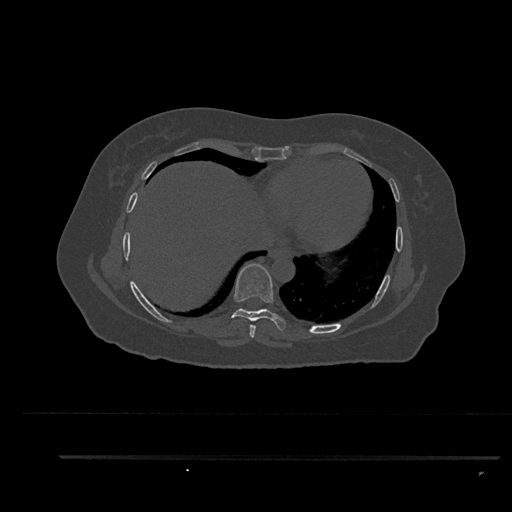
CT including the spine, one axial slice; position 461 of 797 along the scan axis; bone window (W 1800 / L 400 HU); 512 × 512 image matrix. Female patient, age 44 years. From the clinical record (not read from this slice): primary cancer: renal; vertebrae with lytic lesions (as recorded): L1.
Structures marked on this image (semi-automatic segmentation, software-assisted and operator-edited):
- T7 vertebra: bounding box (x1, y1, x2, y2) in pixels: (249, 324, 256, 338)
- T8 vertebra: (231, 264, 286, 331)